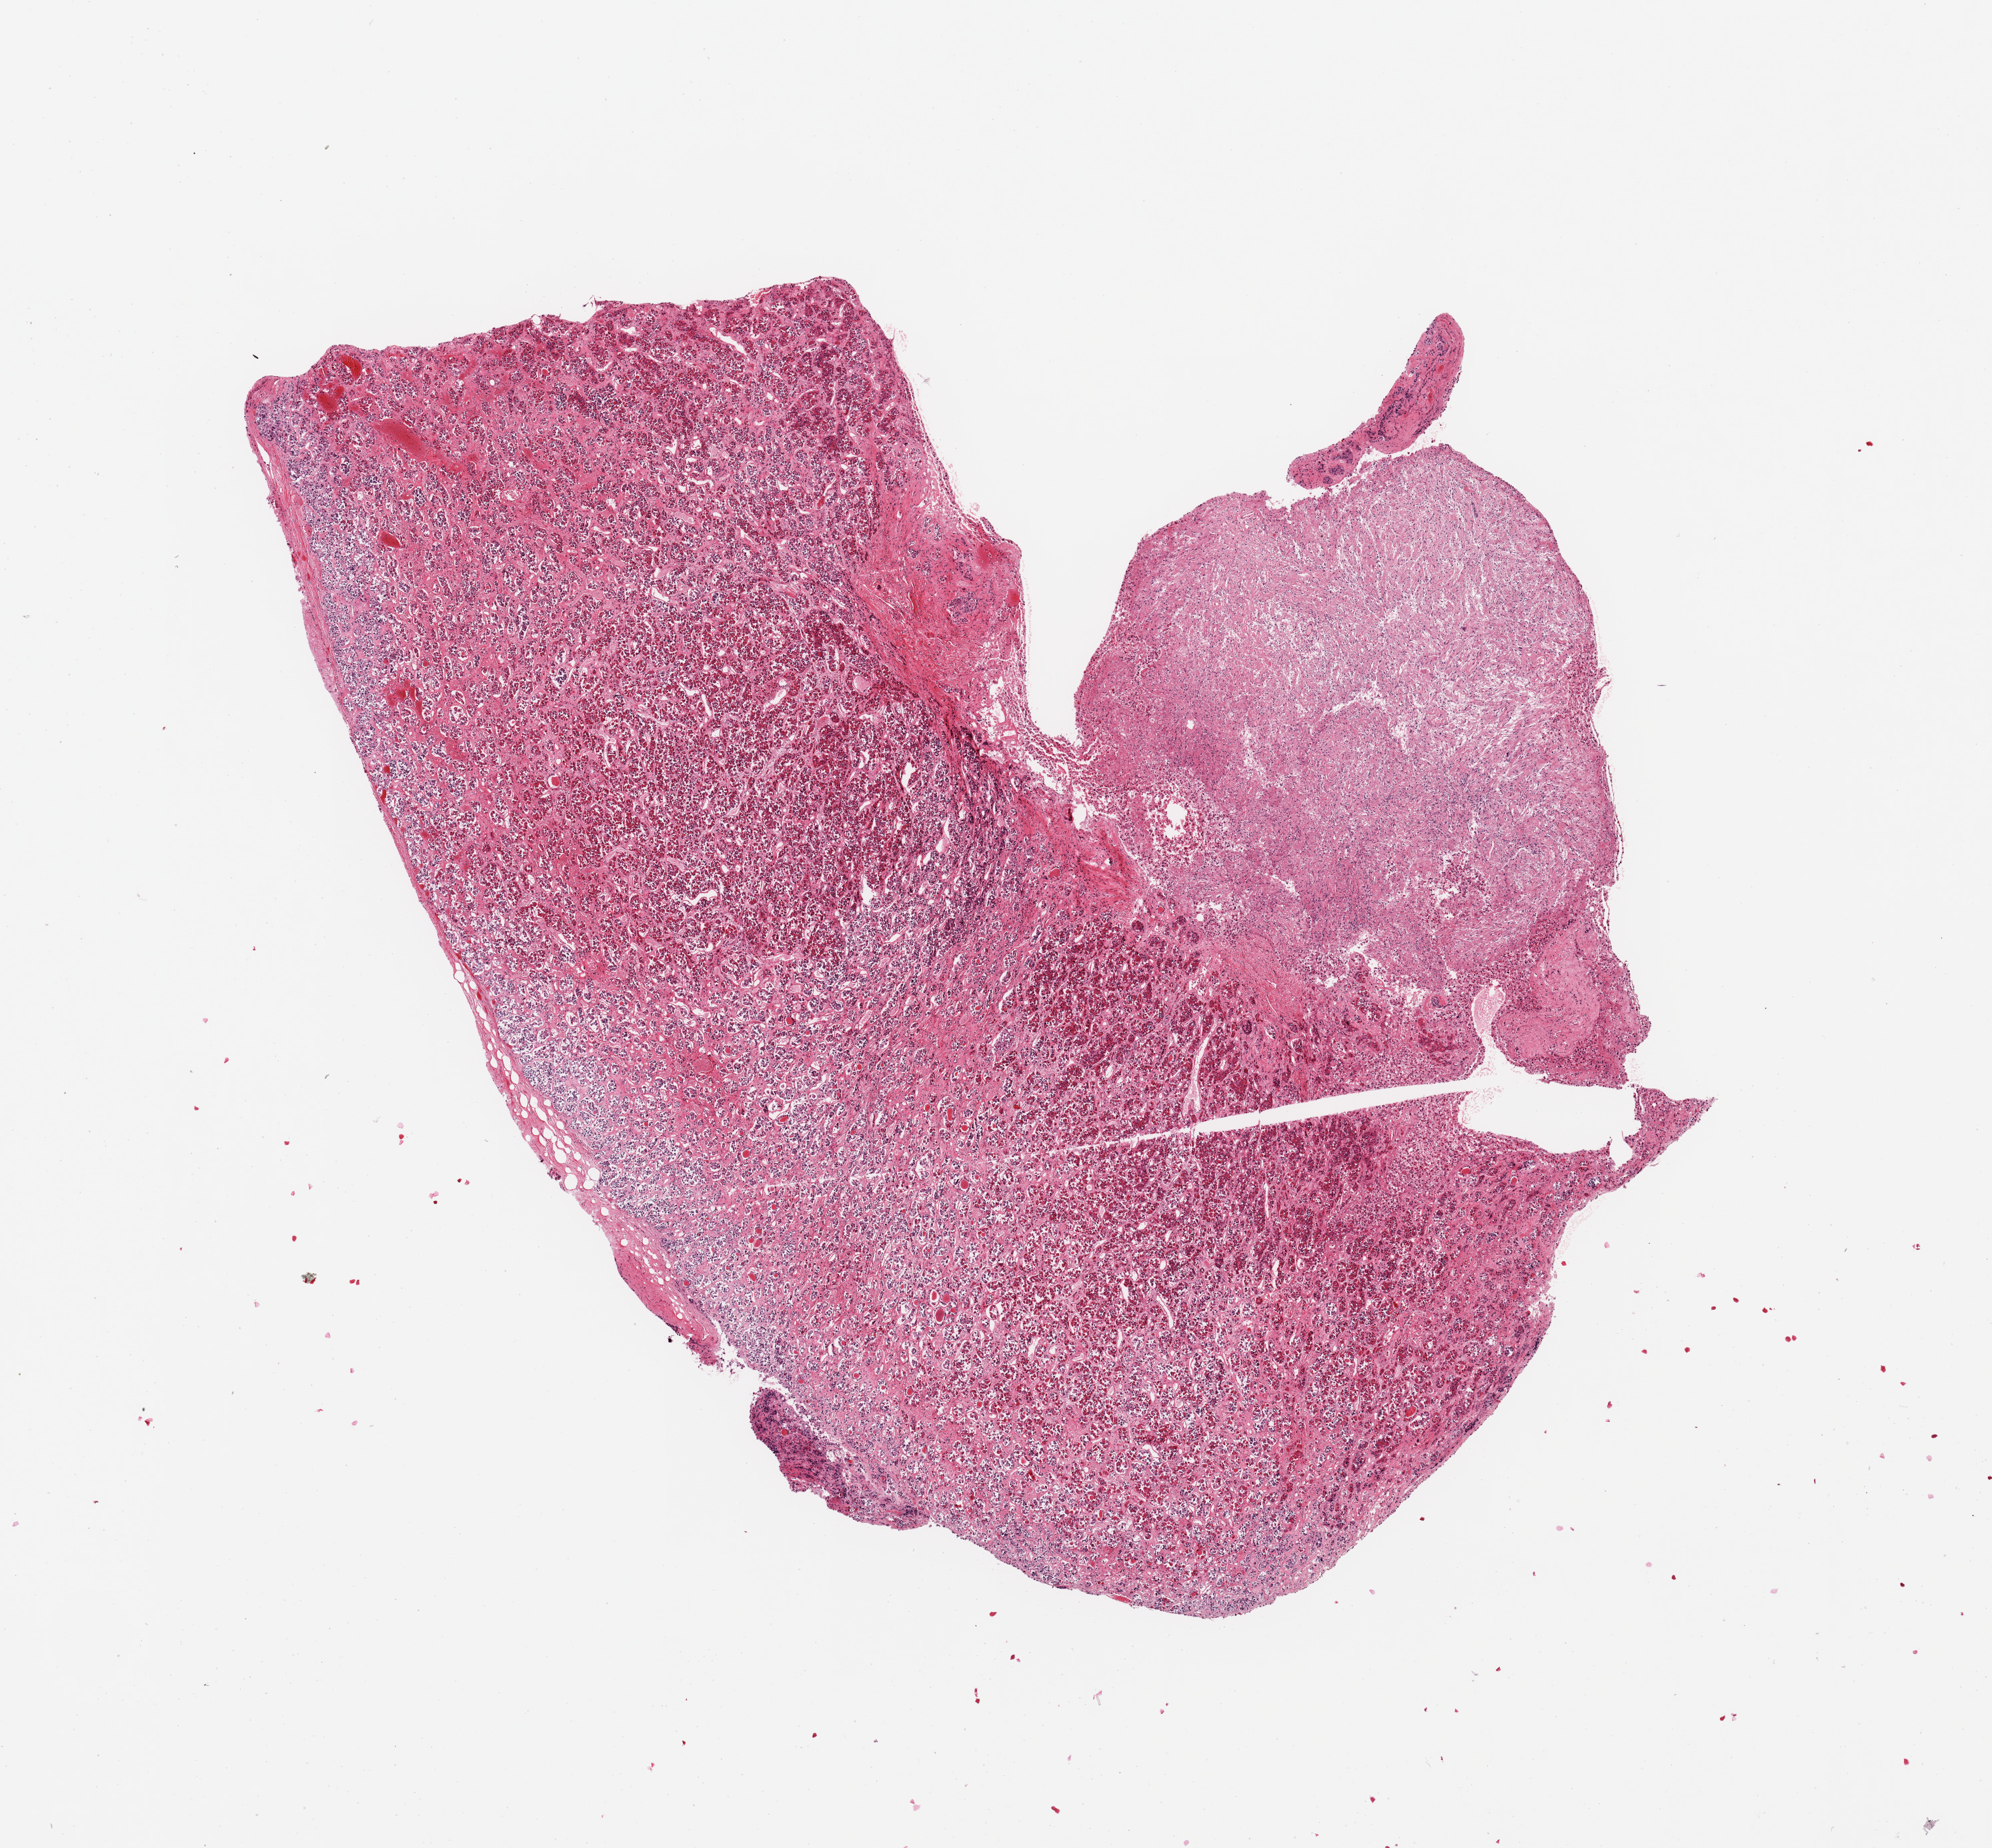
H&E whole-slide image, a low-resolution overview of the entire scanned area, about 11.8 x 11.0 mm; PAXgene-fixed paraffin-embedded (PFPE) section; sampled site (target tissue): pituitary; donor tissue sample.
Pathologist's review note for this sample: 1 piece; adenohypophysis (70%) and neurohypophysis (30%).